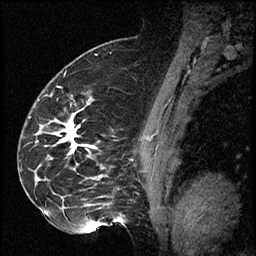
Breast MRI (dynamic contrast-enhanced), one sagittal slice. Position 43 of 60 along the scan axis. Dynamic contrast-enhanced series, image 2 of 2 at this slice position (ordered by acquisition). 1.5 T. TE 4.2 ms, TR 17.3 ms. 256 × 256 image matrix, field of view 200 × 200 mm. Female patient. From the clinical record (not read from this slice): setting: breast cancer imaged before/during neoadjuvant chemotherapy; receptor status: HR-positive, HER2-negative.
Annotated regions visible in this slice (semi-automatically segmented with operator editing):
- analysis volume of interest (the breast-tissue region the enhancement analysis was run in; not a lesion): box from (x=41, y=97) to (x=115, y=223) px
- tumour enhancement mask (voxels above the 100 % enhancement threshold inside the analysis volume of interest): (x=63, y=120)–(x=79, y=153)